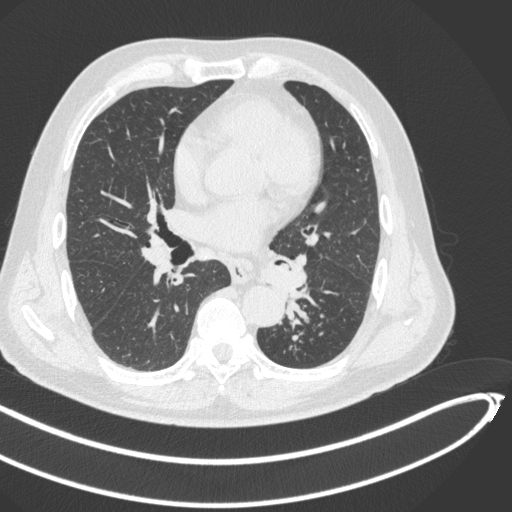
Chest CT, one axial slice; position 239 of 466 along the scan axis; reconstruction kernel B31f; 120 kVp; lung window (W 1500 / L -600 HU); 1 mm slice thickness; 512 × 512 image matrix, field of view 400 × 400 mm. Male patient, age 64 years. From the clinical record (not read from this slice): clinical TNM (as recorded): T1c N0 M0.
Annotated regions visible in this slice (rectangle marked by the reading radiologist):
- lung tumour (recorded histology: squamous cell carcinoma): bounding box (x1, y1, x2, y2) in pixels: (258, 256, 297, 303)